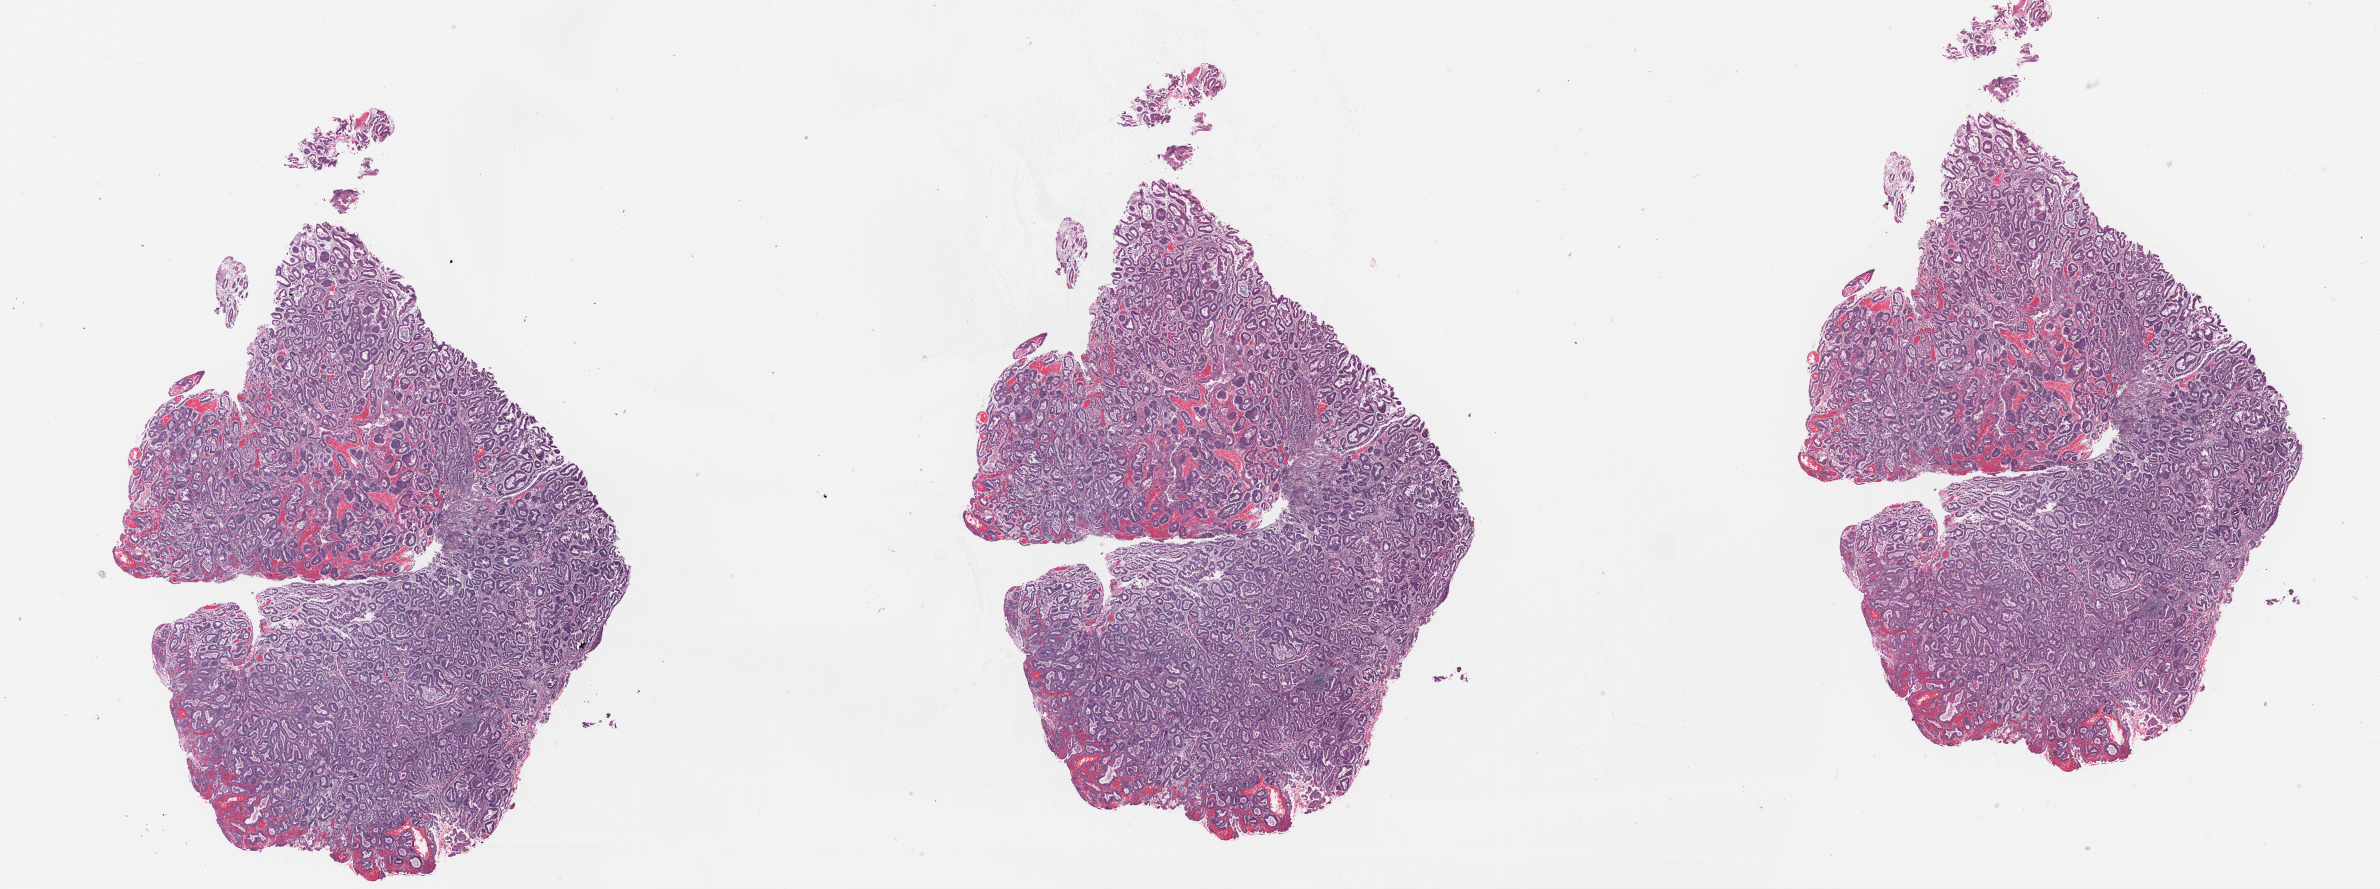
Hematoxylin and eosin (H&E) stained whole-slide image, a low-resolution overview of the entire scanned area, about 37.6 x 14.0 mm (slide scanned at 40x); formalin-fixed paraffin-embedded (FFPE) diagnostic section; primary tumour sample from the uterus. Female, age 70 years at initial diagnosis. Histologic grade: G2 (moderately differentiated).
• FIGO stage: IA
• histologic diagnosis: Endometrioid adenocarcinoma, NOS (endometrium)